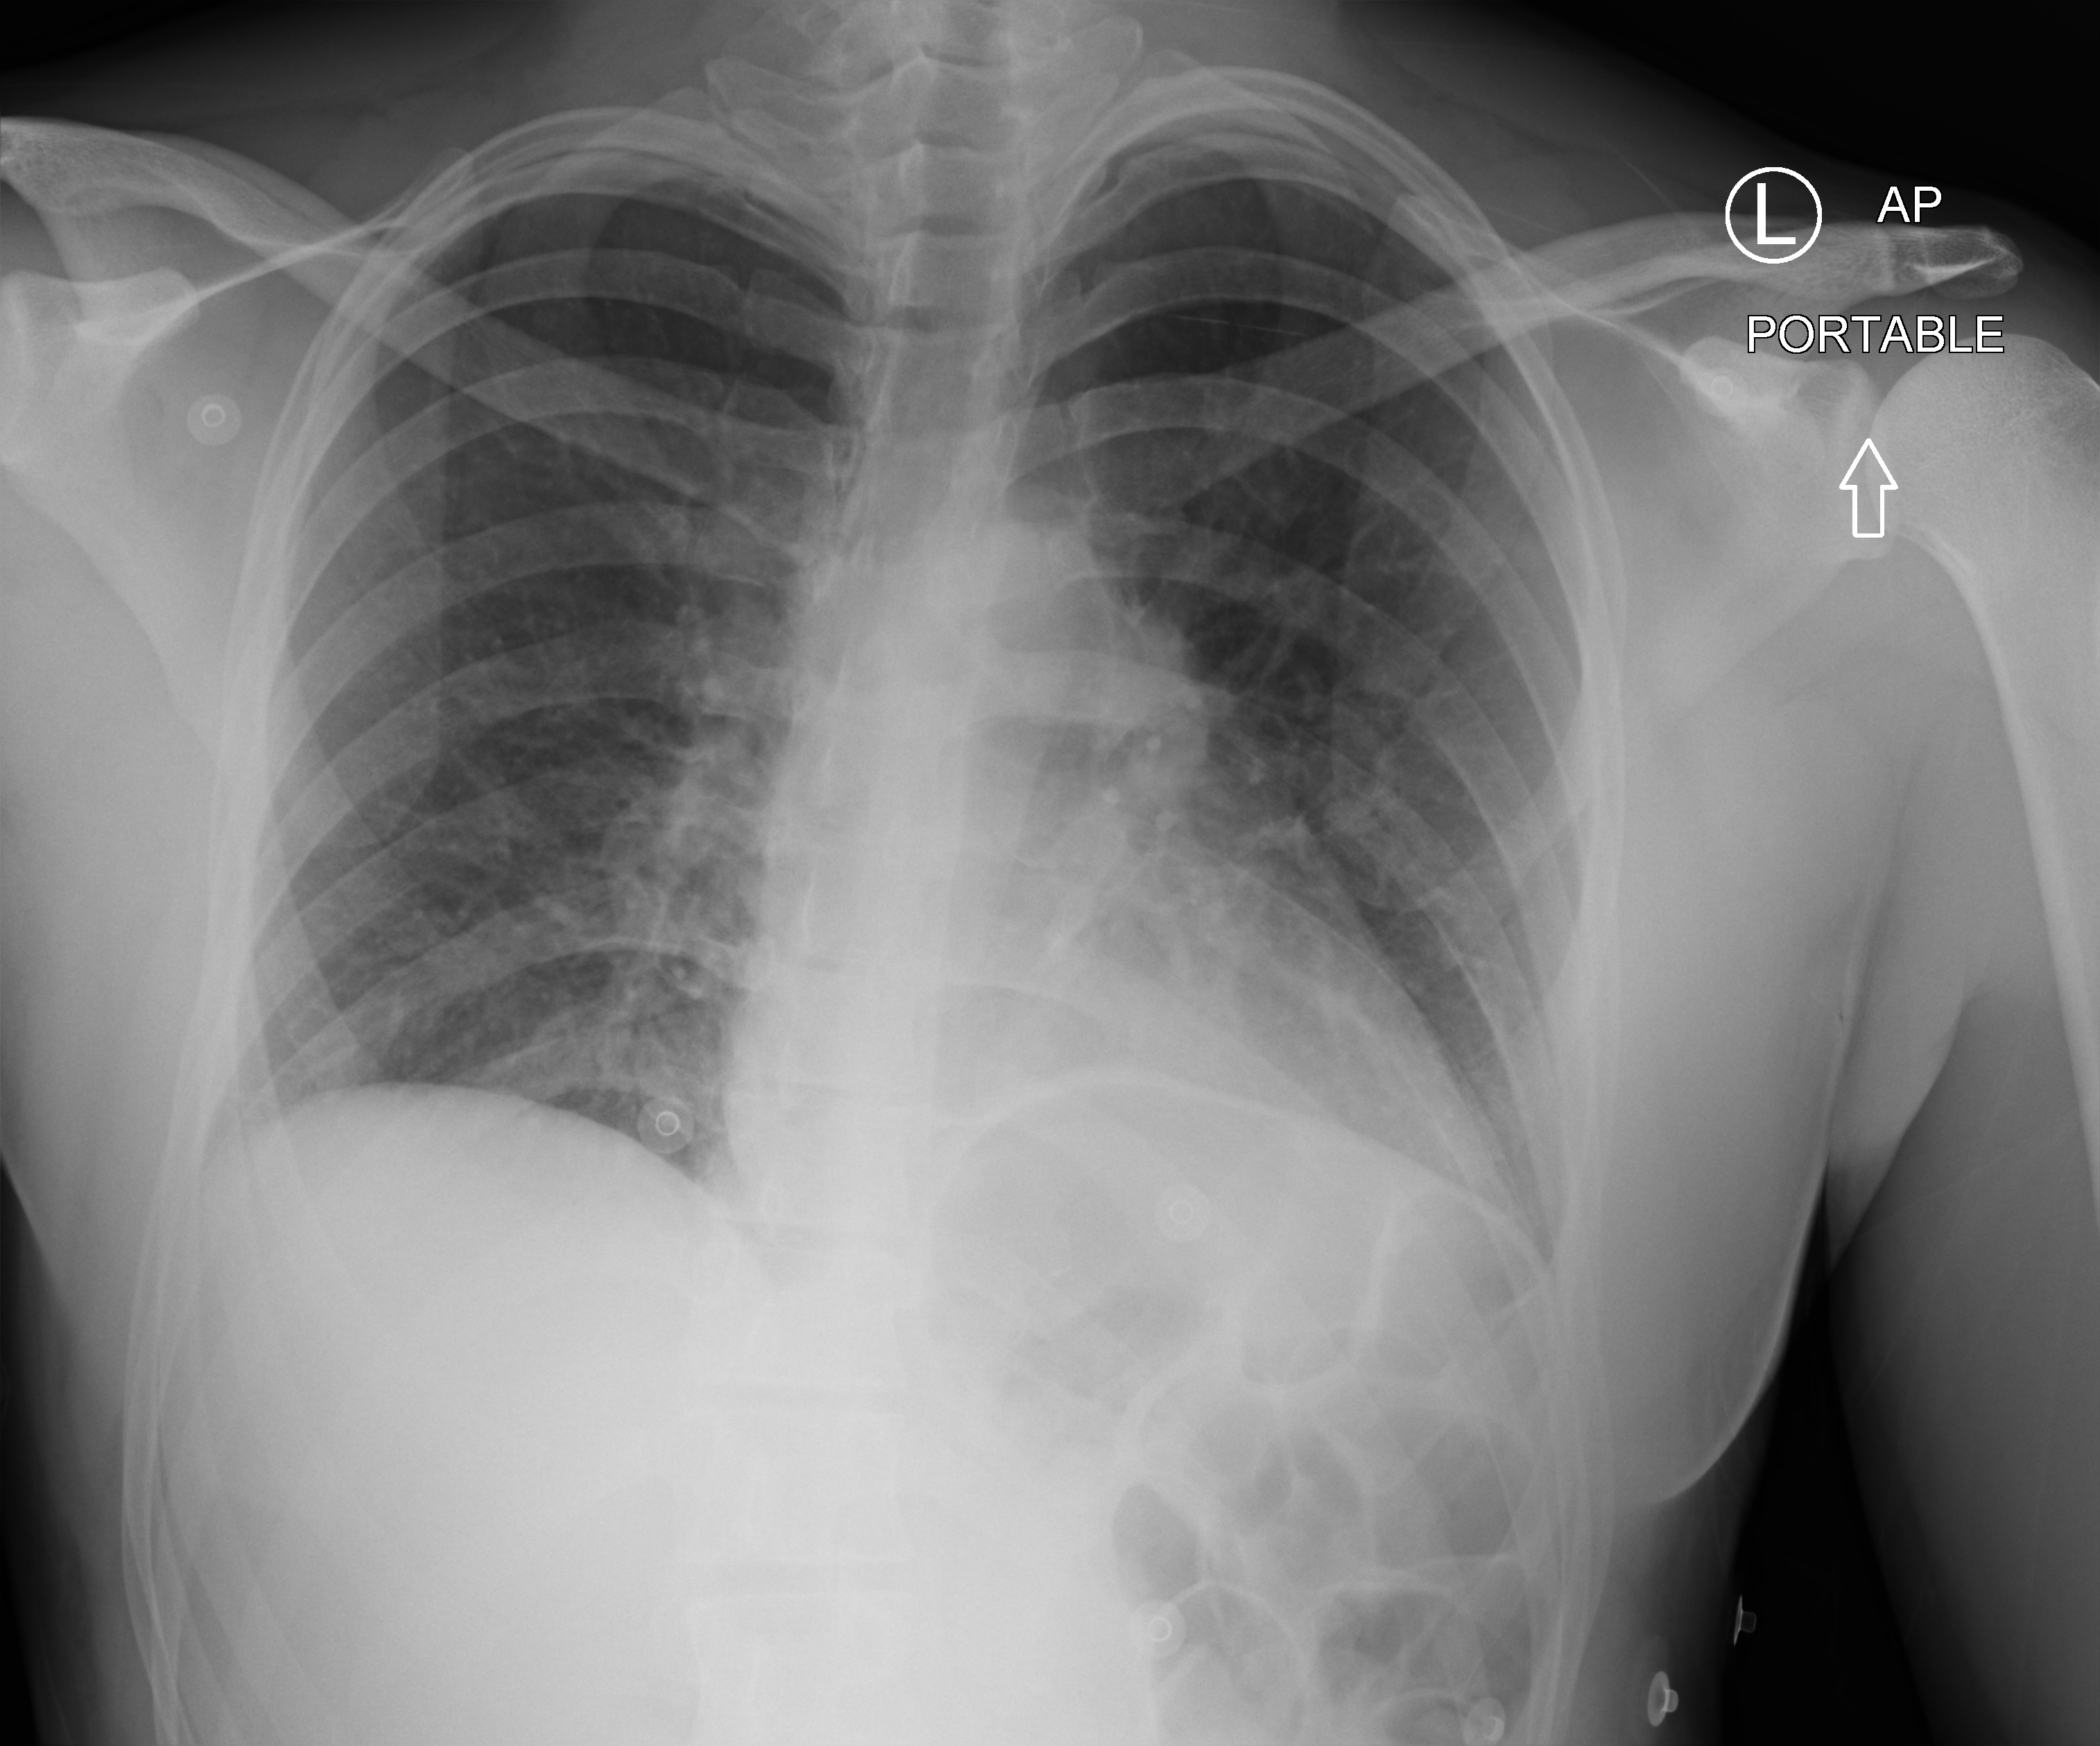
Portable chest radiograph, anteroposterior (AP) projection. Patient hospitalised with COVID-19; male, aged 18–59 years.
Admission-level facts for this patient (not findings on this image; timing relative to this image not recorded):
- admitted to intensive care during this hospital stay: no
- length of hospital stay: 11 days